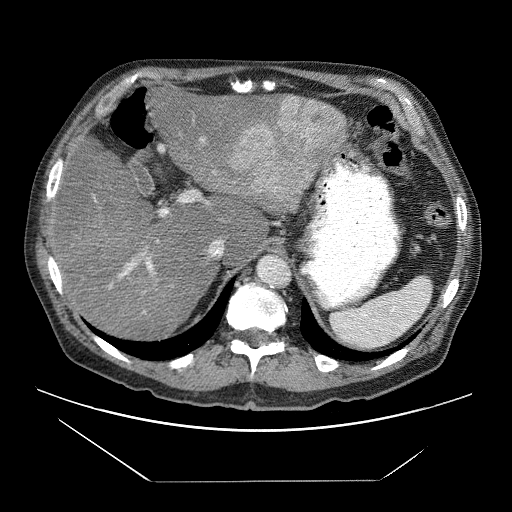
Contrast-enhanced abdominal CT (liver protocol), one axial slice; position 48 of 83 along the scan axis; reconstruction kernel STANDARD; 120 kVp; soft-tissue window (W 400 / L 40 HU); 2.5 mm slice thickness; 512 × 512 image matrix, field of view 420 × 420 mm. From the clinical record (not read from this slice): diagnosis: hepatocellular carcinoma (patient treated with transarterial chemoembolisation; whether this scan precedes or follows treatment is not stated here); TNM stage (as recorded): Stage-IVB; Child-Pugh class: B; tumour differentiation: poorly differentiated.
Structures marked on this image (semi-automatic segmentation, software-assisted and operator-edited):
- liver parenchyma outside the tumour (the mass and vessels are separate outlines, so this box may not span the whole liver): bounding box <48,77,346,338> (left, top, right, bottom; pixels)
- mass: <230,97,348,209>
- liver vessels: <95,137,215,313>